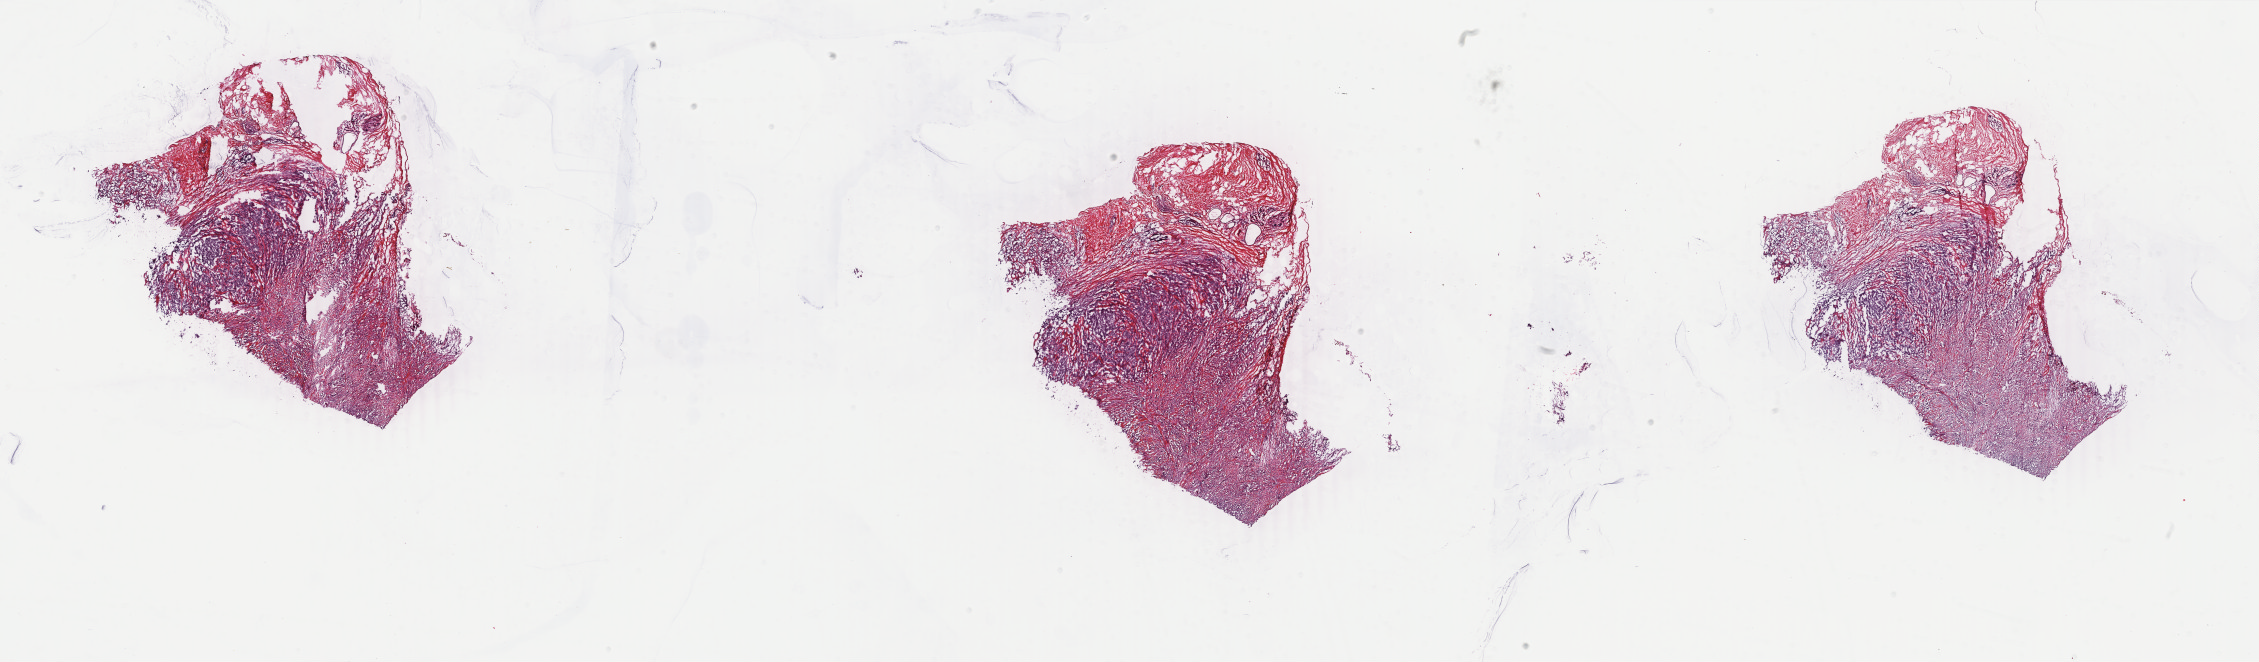
Whole-slide histology image, H&E-stained, a low-resolution overview of the entire scanned area, about 35.9 x 10.5 mm (from a 40x scan), frozen section, sample: primary tumour, breast. Patient: female, age at initial diagnosis 61 years. Pathologist review of this section (percent, as recorded): tumour cells 75%, tumour nuclei 75%, normal cells 0%, stromal cells 23%, necrosis 2%. Infiltration values recorded for this section: lymphocyte infiltration 3%, monocyte infiltration 0%, neutrophil infiltration 0%.
Laterality: right. Diagnosis: Lobular carcinoma, NOS. AJCC pathologic stage: IIA. TNM: T2 N0 (i+) M0.